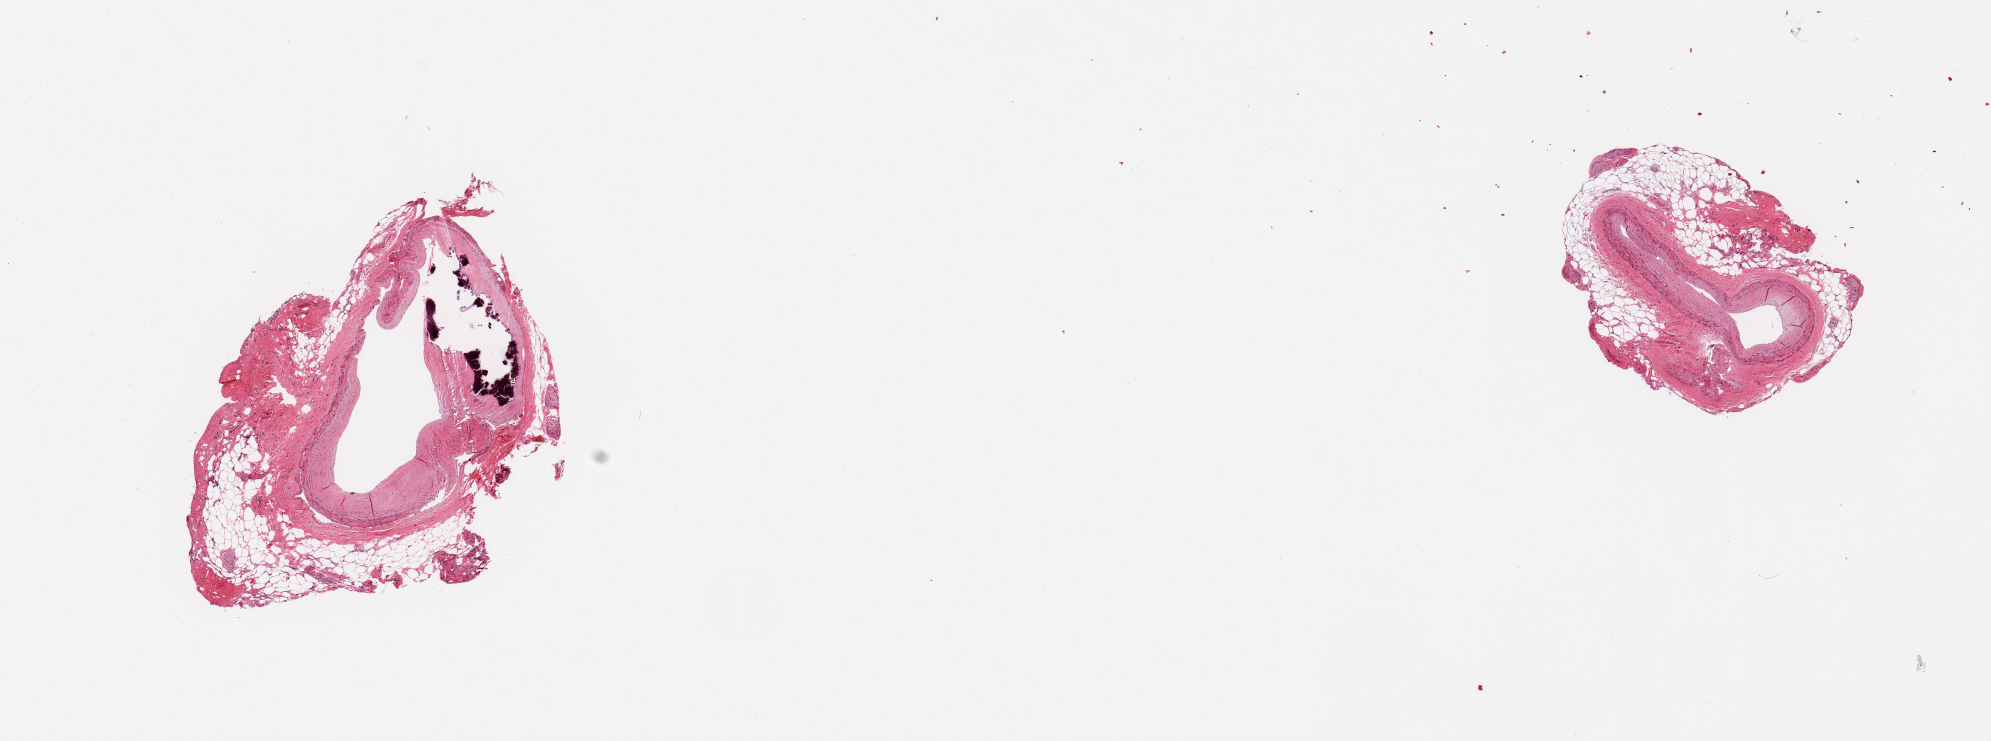
Digitized H&E-stained section, whole scanned area (about 15.8 x 5.9 mm) shown as a low-resolution overview; PAXgene-fixed paraffin-embedded (PFPE) section; target tissue: coronary artery; donor tissue sample. Male donor.
Review note (as recorded): 2 pieces; 1.3 mm calcific plaque; 40% external fat.